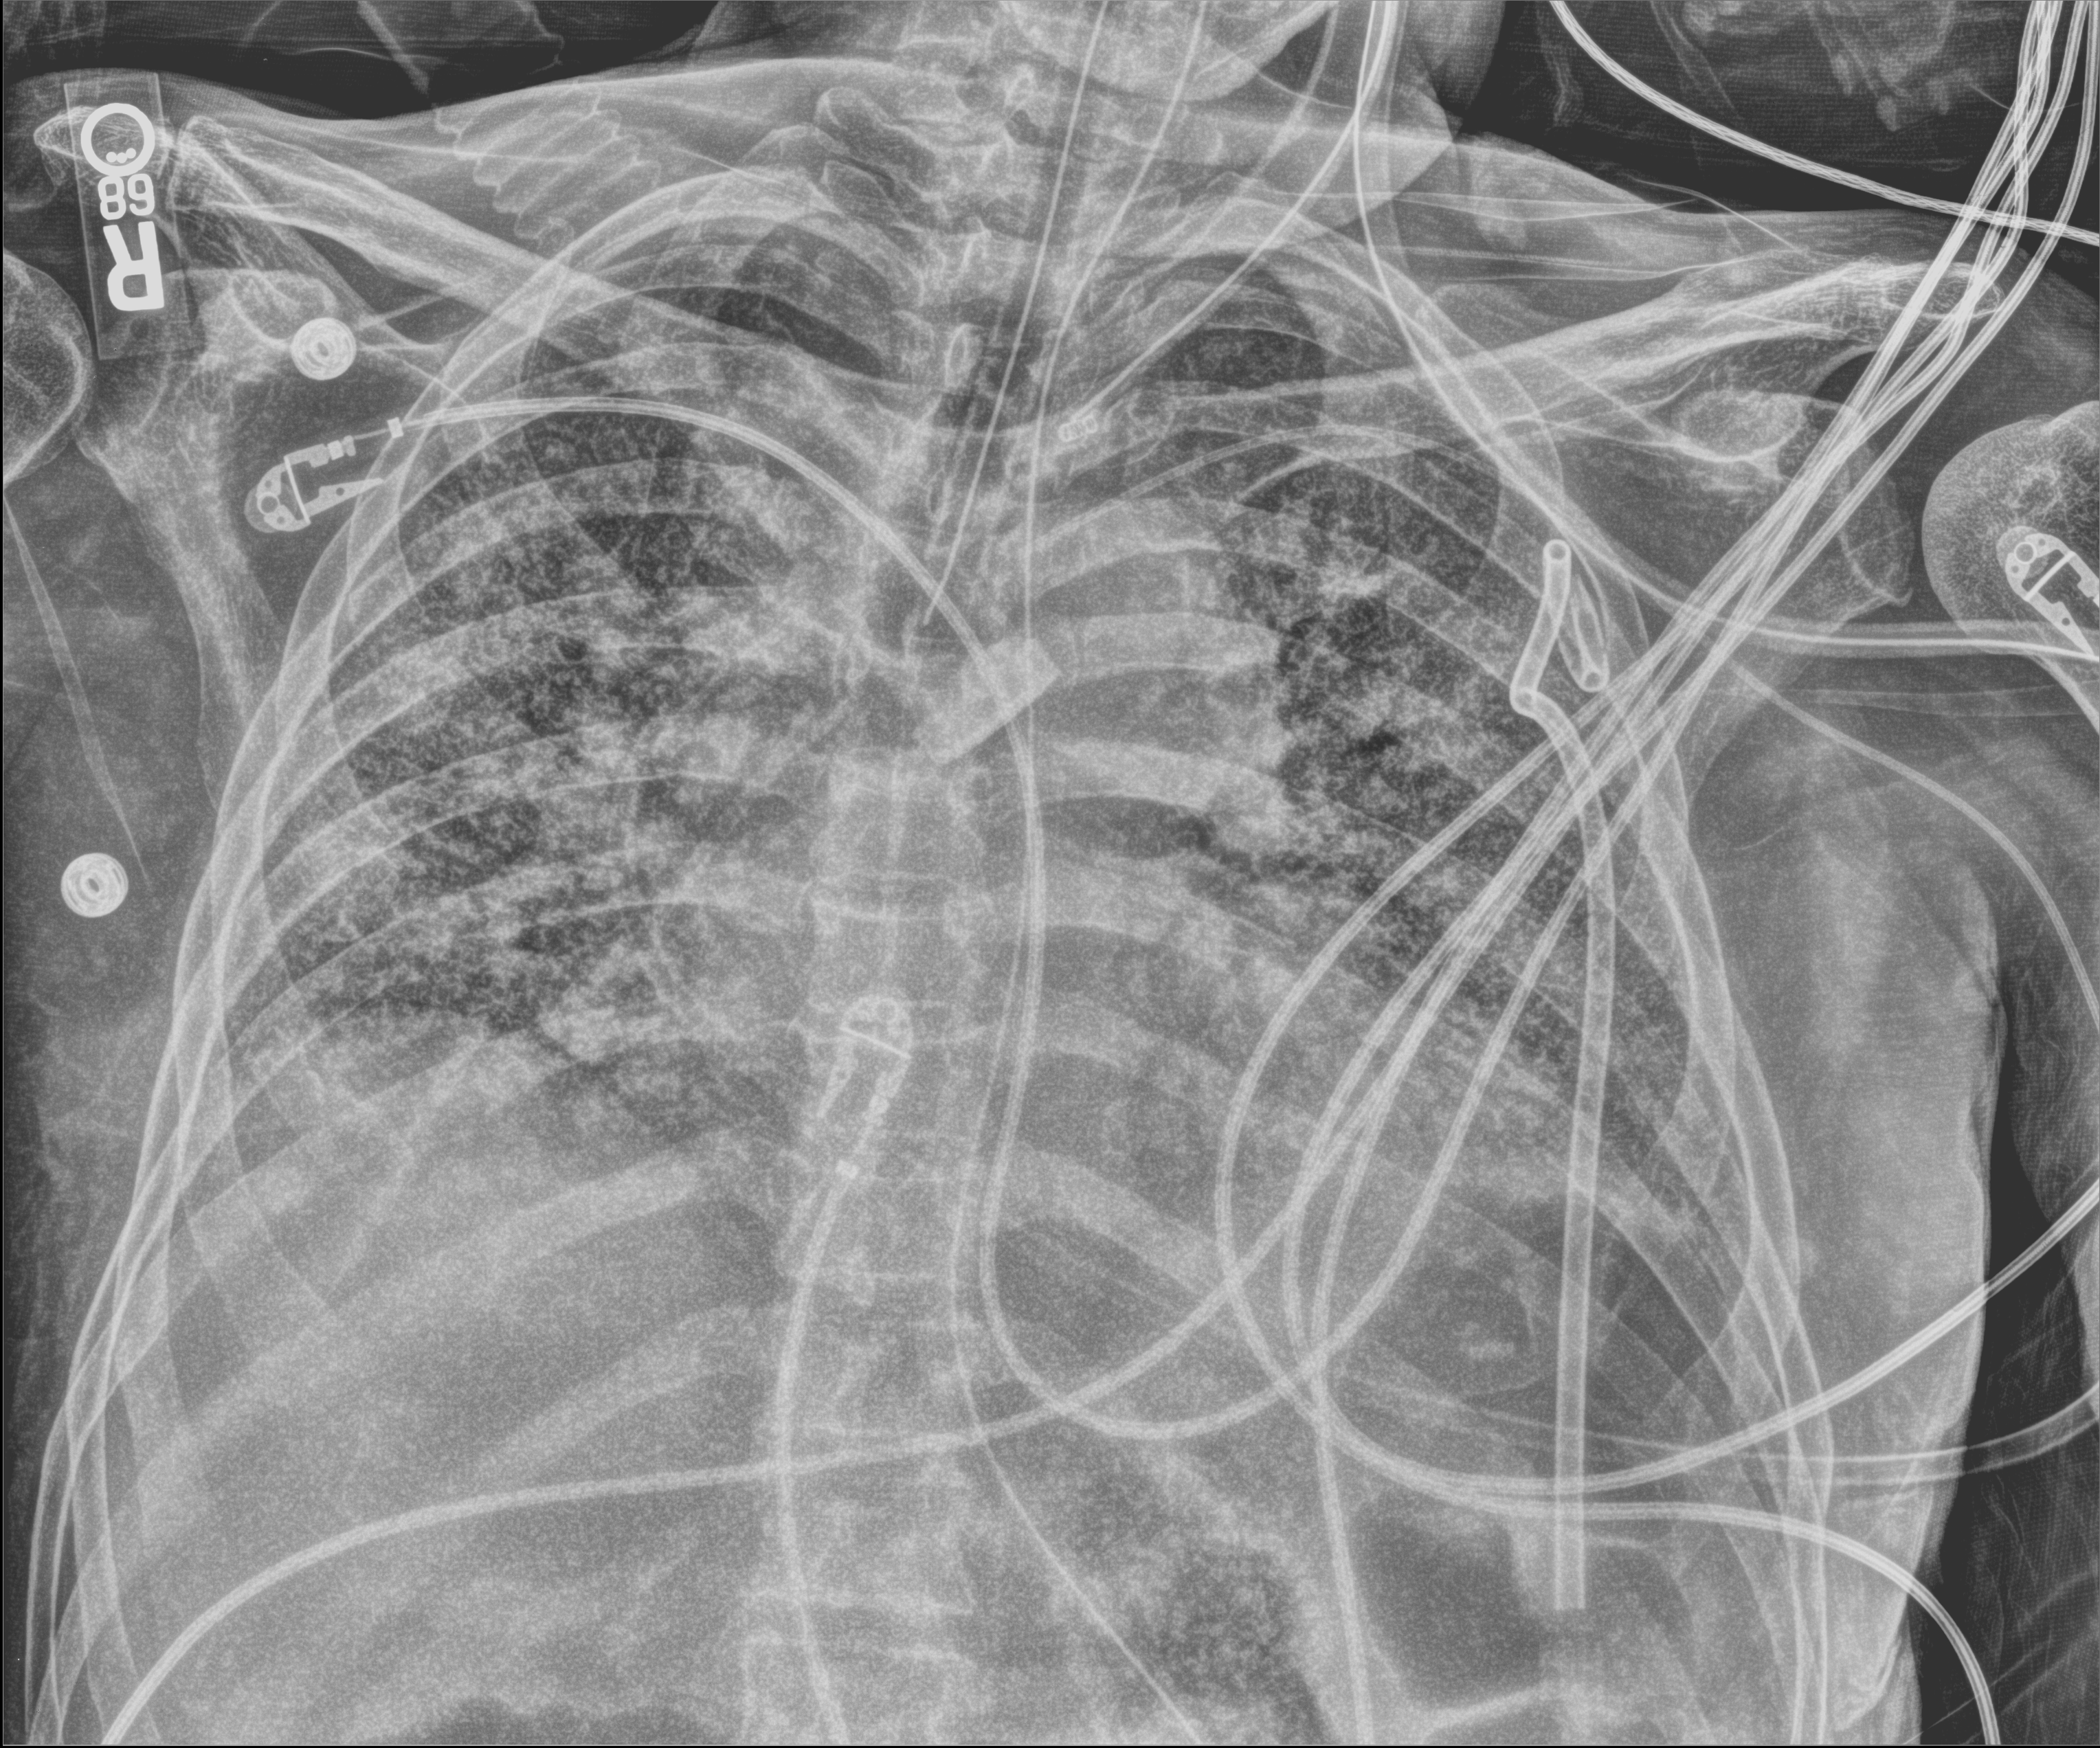
Portable chest radiograph; anteroposterior (AP) projection. Male patient hospitalised with COVID-19, age 60–74 years.
Admission-level facts for this patient (not findings on this image; timing relative to this image not recorded):
- mechanically ventilated during this hospital stay: yes